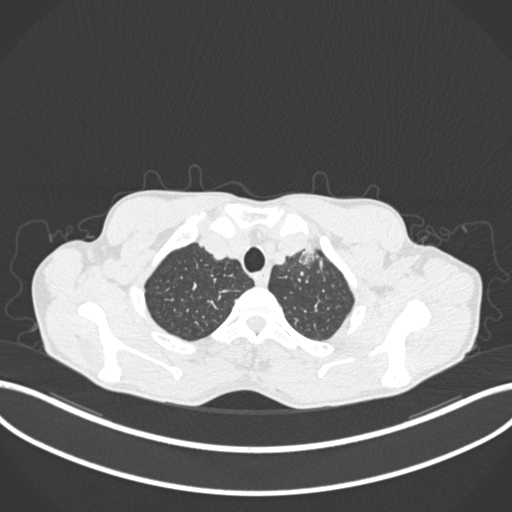
Chest CT, one axial slice. Slice 183 of 211 in the series (ordered by position). 120 kVp. Lung window (W 1500 / L -600 HU). 1 mm slice thickness. 512 × 512 image matrix, field of view 400 × 400 mm. Patient: male, 58 years. From the clinical record (not read from this slice): clinical TNM (as recorded): T1c N1 M0.
Annotated regions visible in this slice (bounding box drawn by a radiologist):
- lung tumour (recorded histology: adenocarcinoma): bounding box [x1, y1, x2, y2] px = [292, 237, 323, 265]